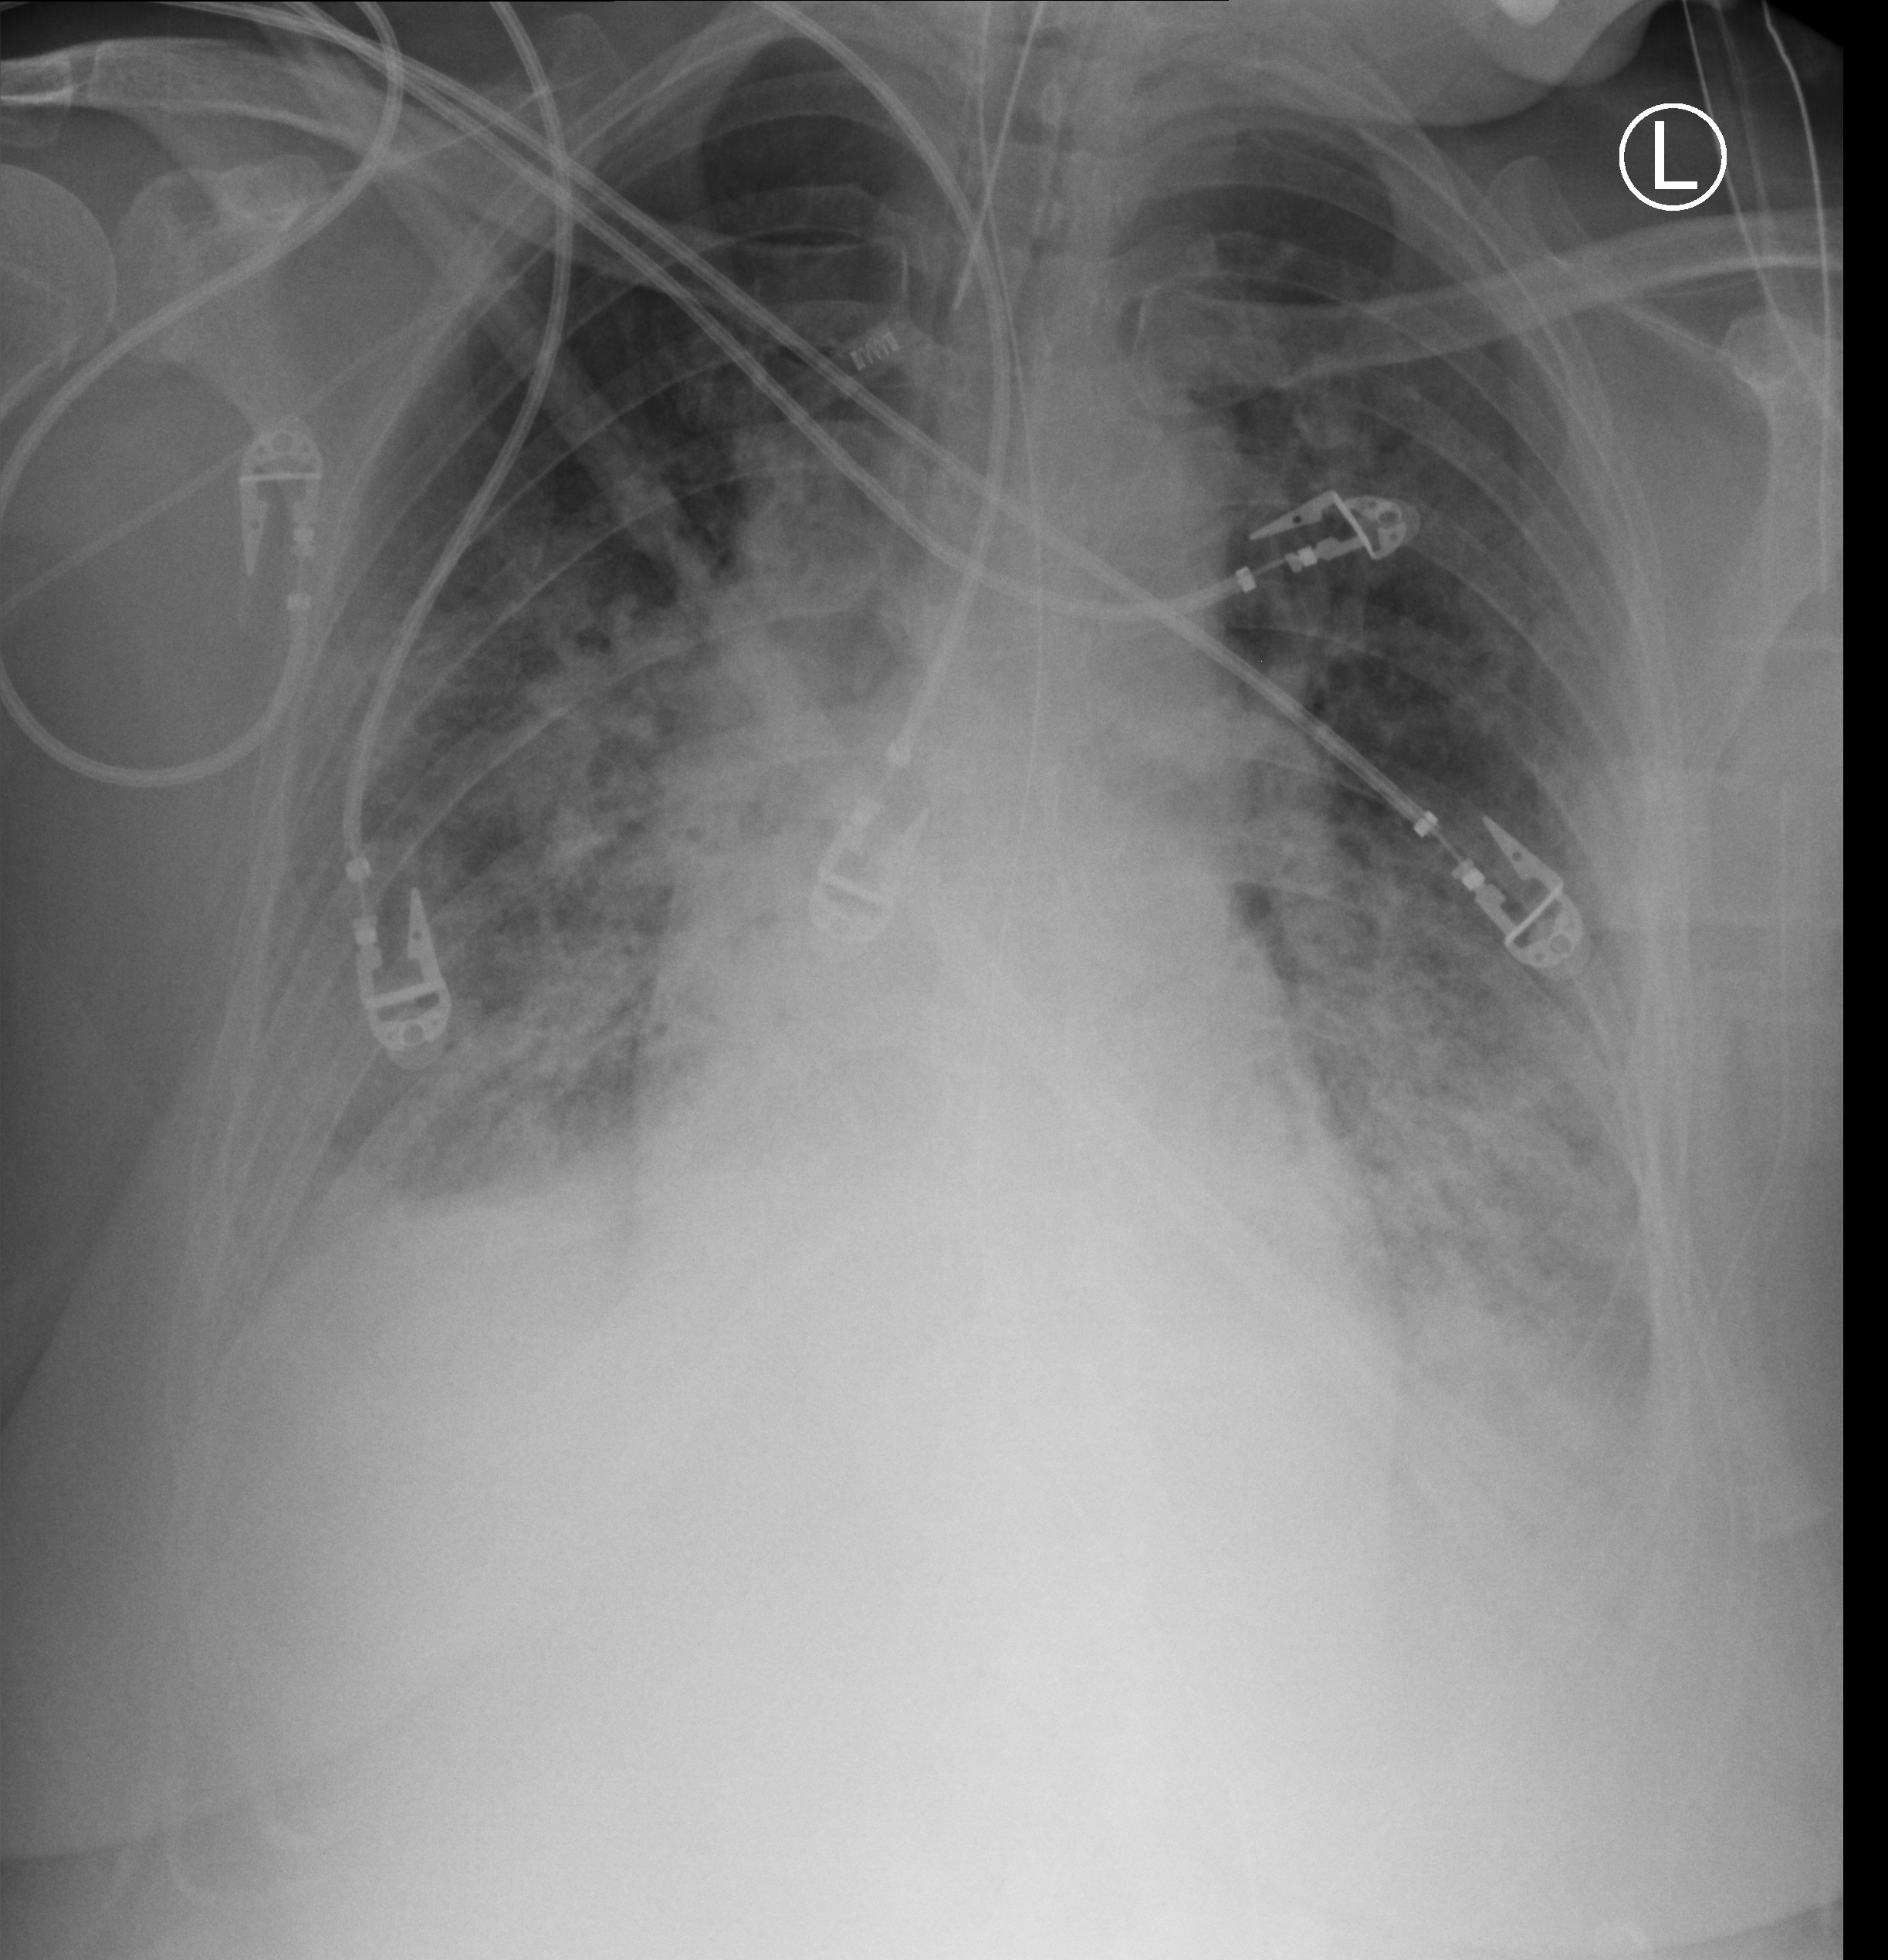
Chest X-ray (portable), anteroposterior (AP) projection. Female patient hospitalised with COVID-19, age 18–59 years.
Admission-level facts for this patient (not findings on this image; timing relative to this image not recorded):
- mechanically ventilated during this hospital stay: yes
- smoking status (admission record): never